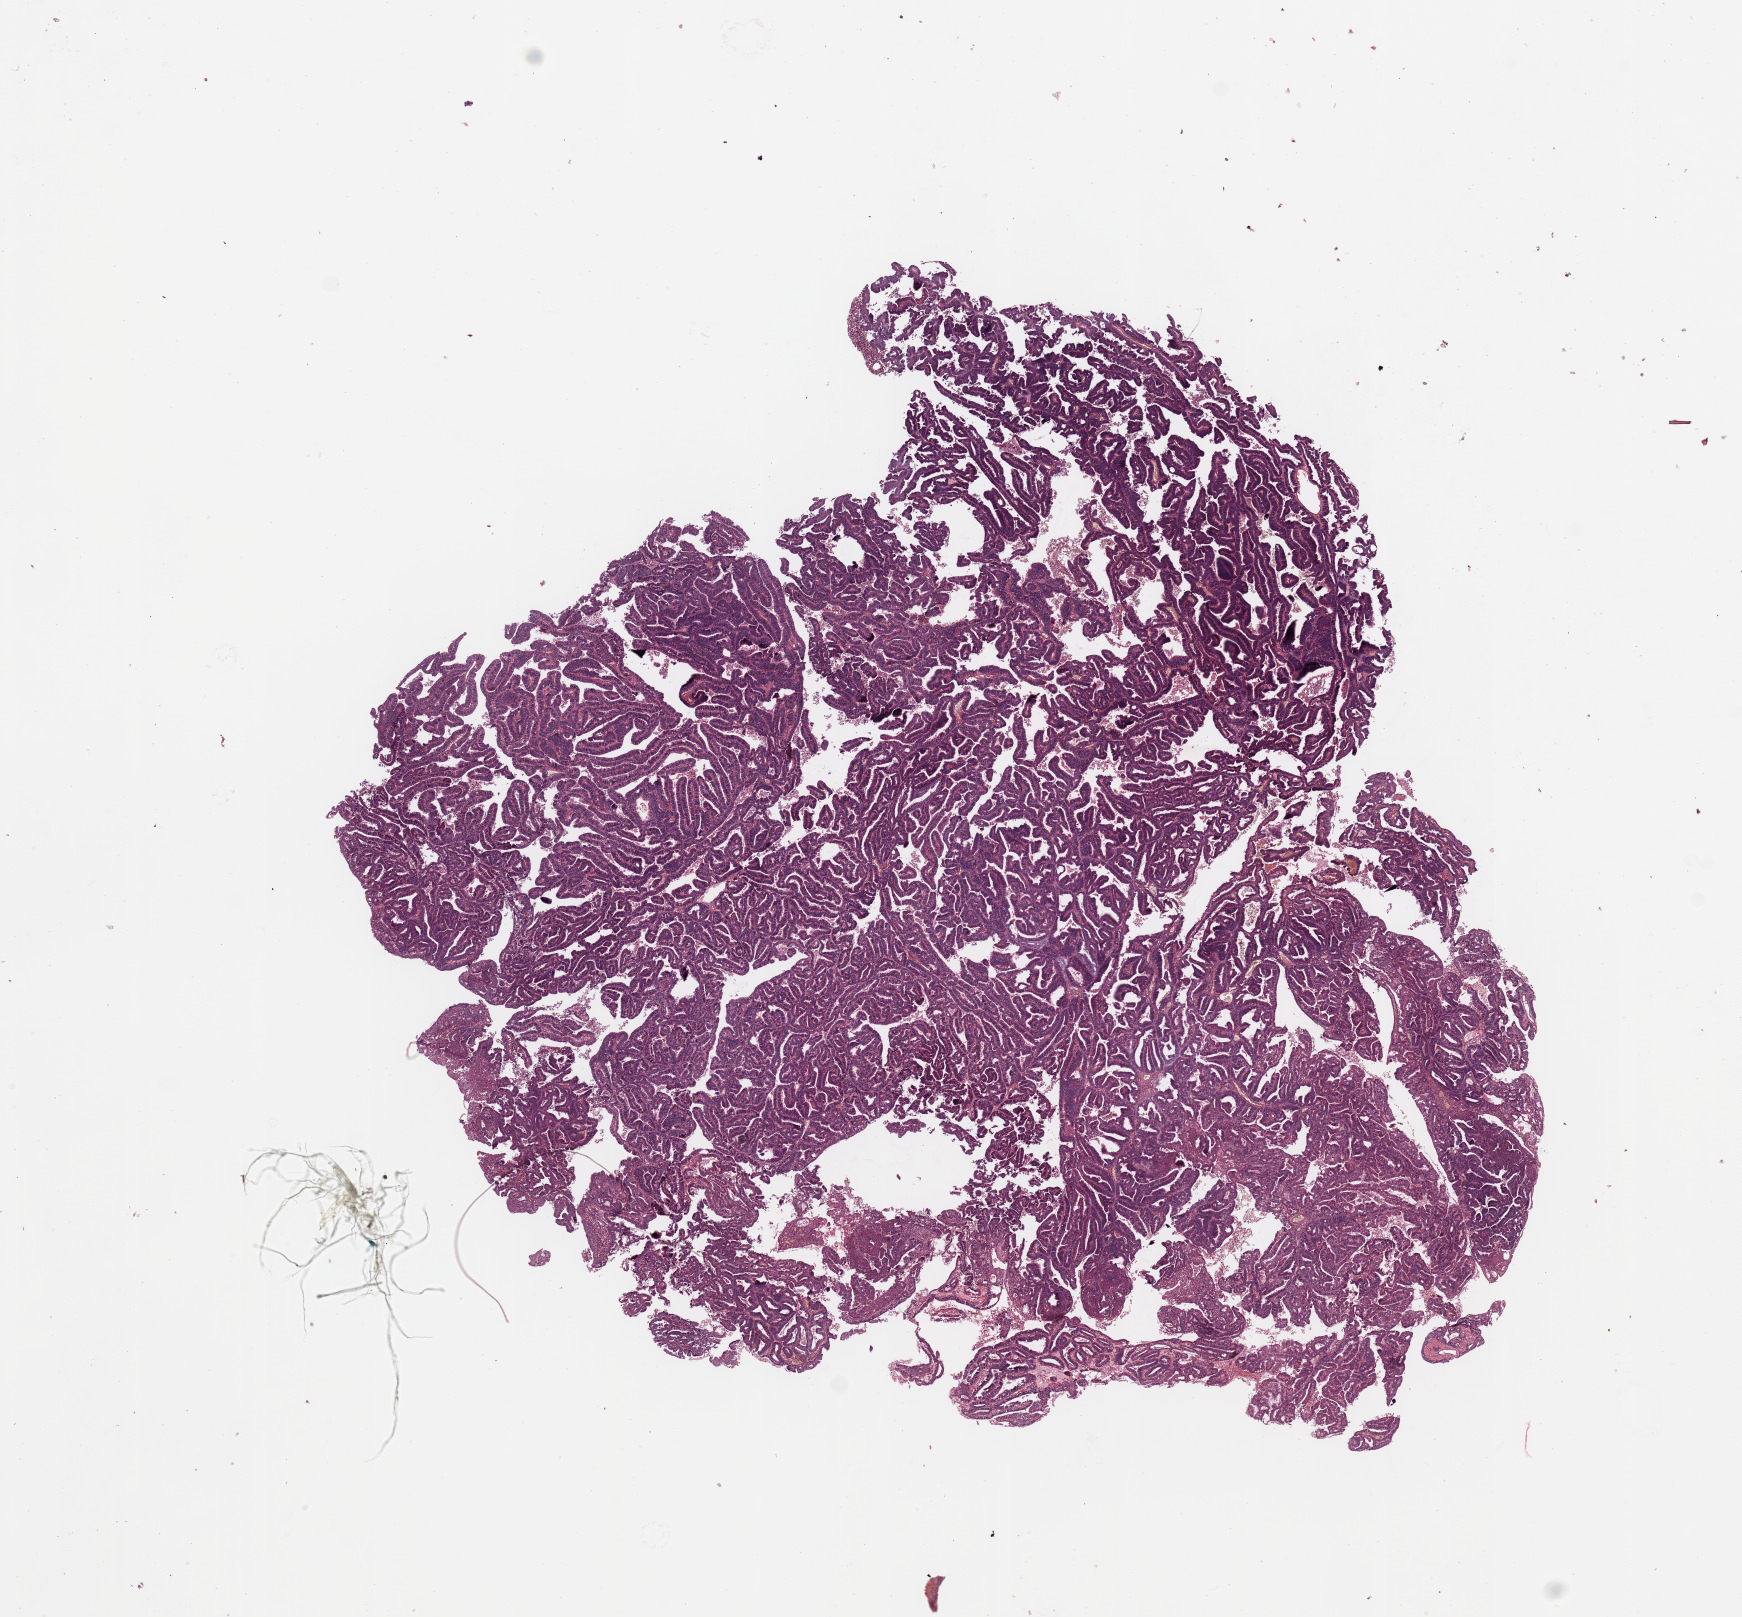
H&E-stained whole-slide image, shown as a low-resolution overview of the whole scanned area (about 13.8 x 12.8 mm), uterus, tissue type not recorded.
Patient diagnosis (cohort enrolment): corpus endometrial carcinoma (uterus).